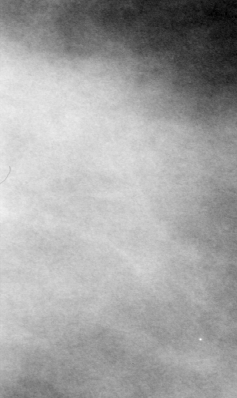
Crop from a digitized film mammogram around one marked abnormality; left breast; CC view.
- Finding: mass, shape round, margins microlobulated; BI-RADS assessment category 3; benign without callback (not worked up further).